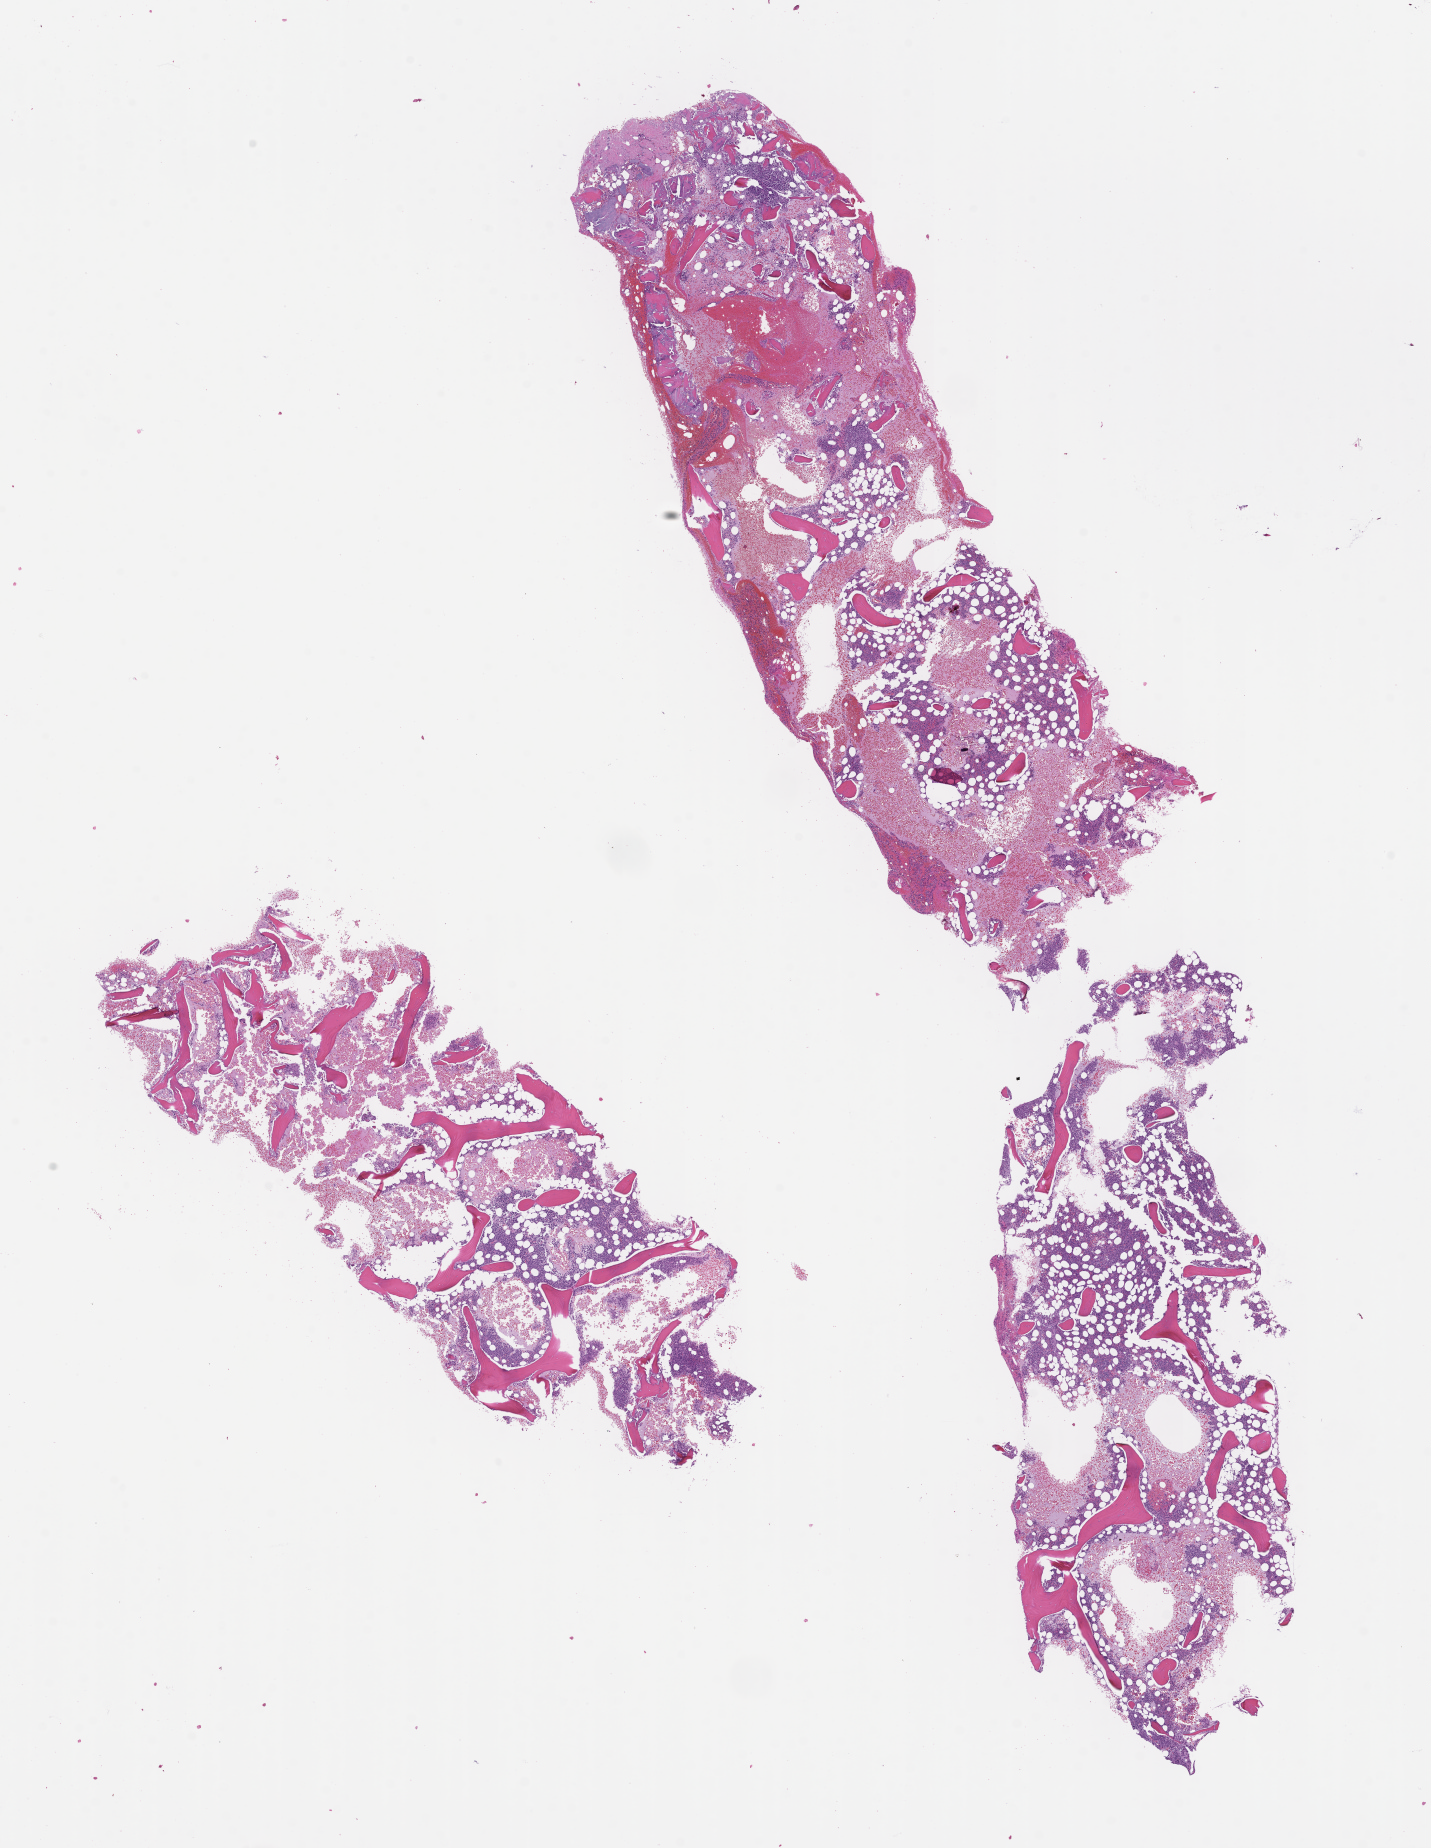
Digitized hematoxylin and eosin (H&E)-stained section — shown as a low-resolution overview of the whole scanned area (about 11.6 x 14.9 mm), formalin-fixed, paraffin-embedded (FFPE) tissue, site: bone marrow. Patient sex: male.
This section: primary tumour tissue. Diagnosis: Plasma Cell Myeloma.